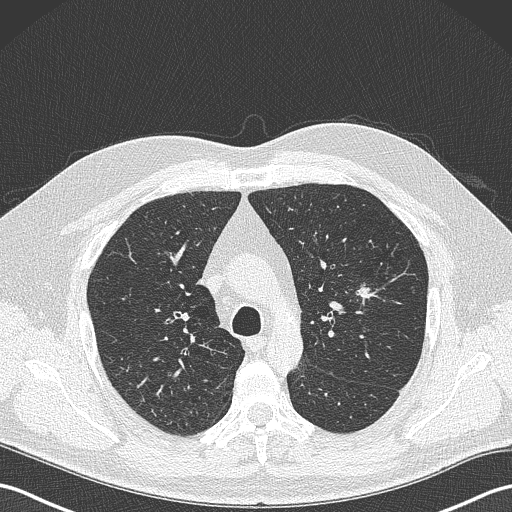
Axial slice from a low-dose chest CT screening exam; baseline annual screen; lung window (W 1500 / L -600 HU); lung (sharp) reconstruction kernel (B50f); 512 × 512 image matrix. Male participant, aged 61 years at enrolment. Former smoker at enrolment.
Expert reader's lesion annotation, bounding box <337,273,387,319> (left, top, right, bottom; pixels). The screening reader recorded 2 non-calcified nodules or masses ≥4 mm on this exam; which of them this box marks is not recorded. Official screen result: positive, change unspecified: nodule(s) >= 4 mm or enlarging nodule(s), mass(es), or other non-specific abnormalities suspicious for lung cancer. Participant outcome: lung cancer diagnosed 160 days after this screen — adenocarcinoma, NOS, left upper lobe, poorly differentiated (G3), stage IA (AJCC 6th edition), 28 mm at pathology.